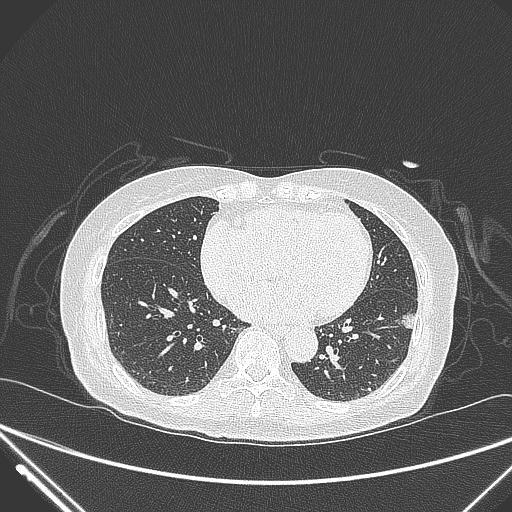
Chest CT, one axial slice; position 116 of 310 along the scan axis; 120 kVp; lung window (W 1500 / L -600 HU); 1 mm slice thickness; 512 × 512 image matrix, field of view 377 × 377 mm. Female patient, age 82 years. From the clinical record (not read from this slice): clinical TNM (as recorded): T1c N0 M0; histopathological grade: G2.
Annotated regions visible in this slice (rectangle marked by the reading radiologist):
- lung tumour (recorded histology: adenocarcinoma): bounding box [x1, y1, x2, y2] px = [398, 307, 413, 335]